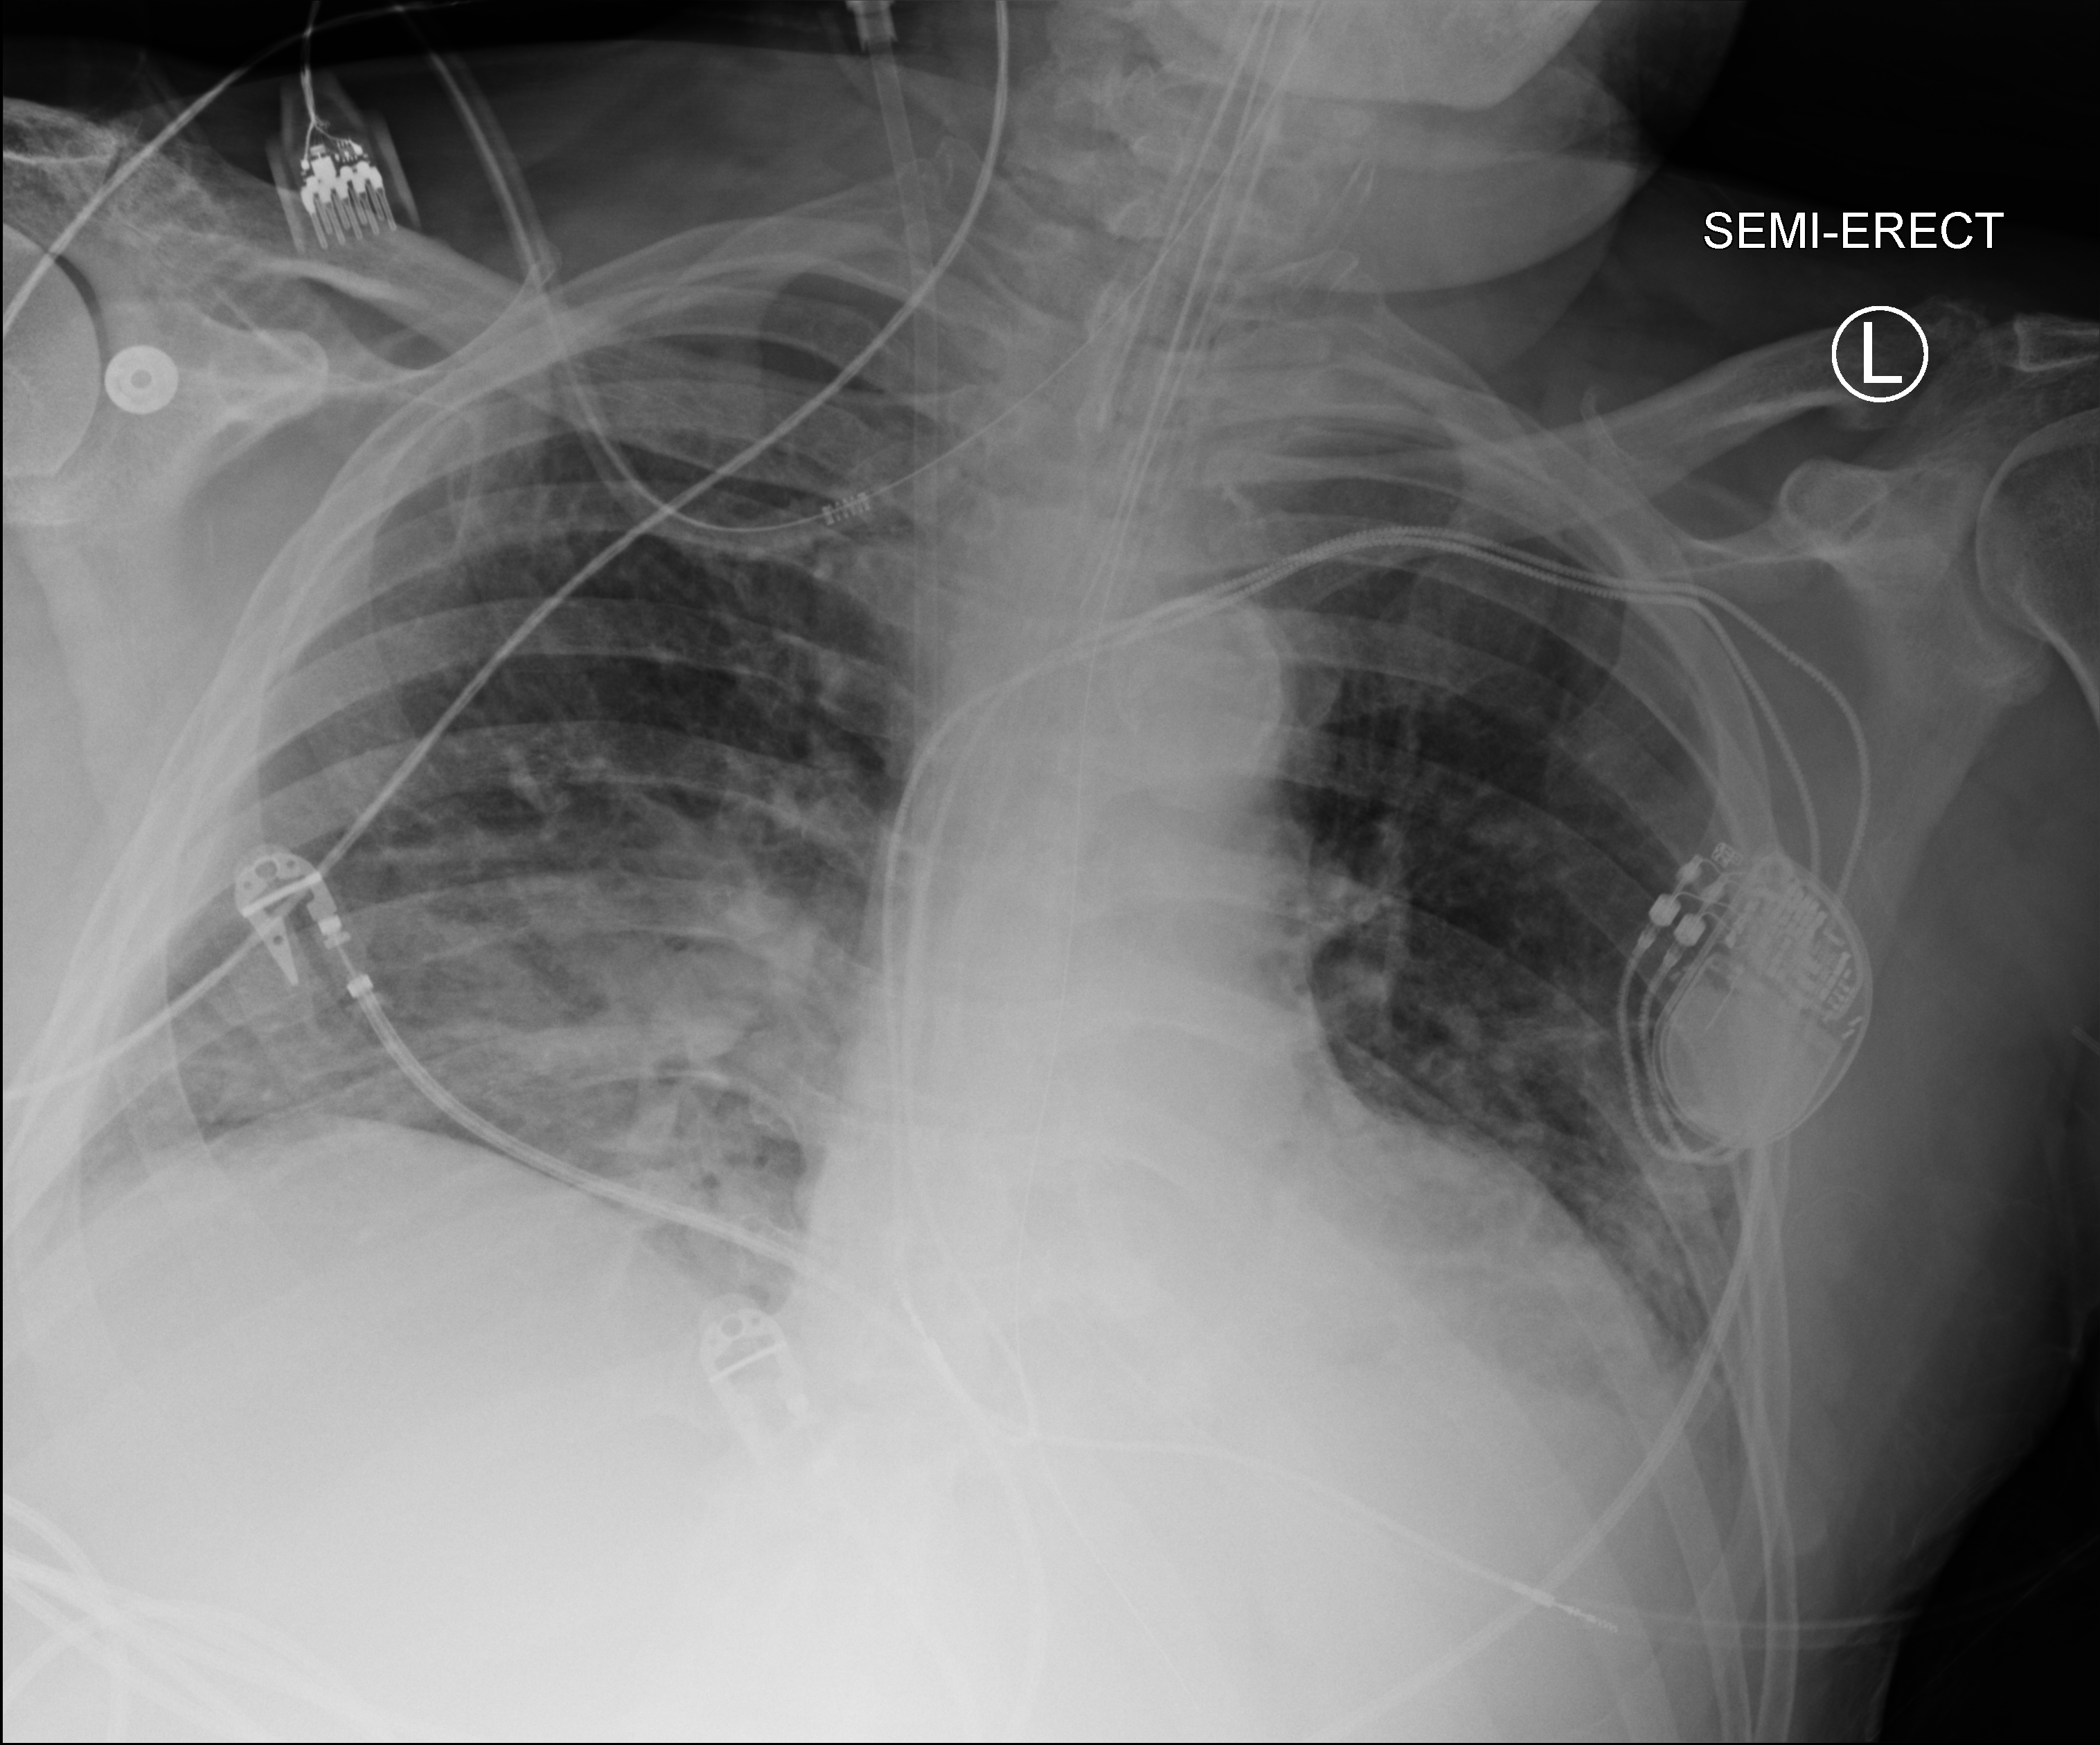
Bedside chest radiograph (computed radiography); anteroposterior (AP) projection. Patient hospitalised with COVID-19; male, aged 60–74 years.
From the hospital-stay record, not from the radiograph (when in the stay this image was taken is not recorded):
- admitted to intensive care during this hospital stay: yes
- mechanically ventilated during this hospital stay: yes